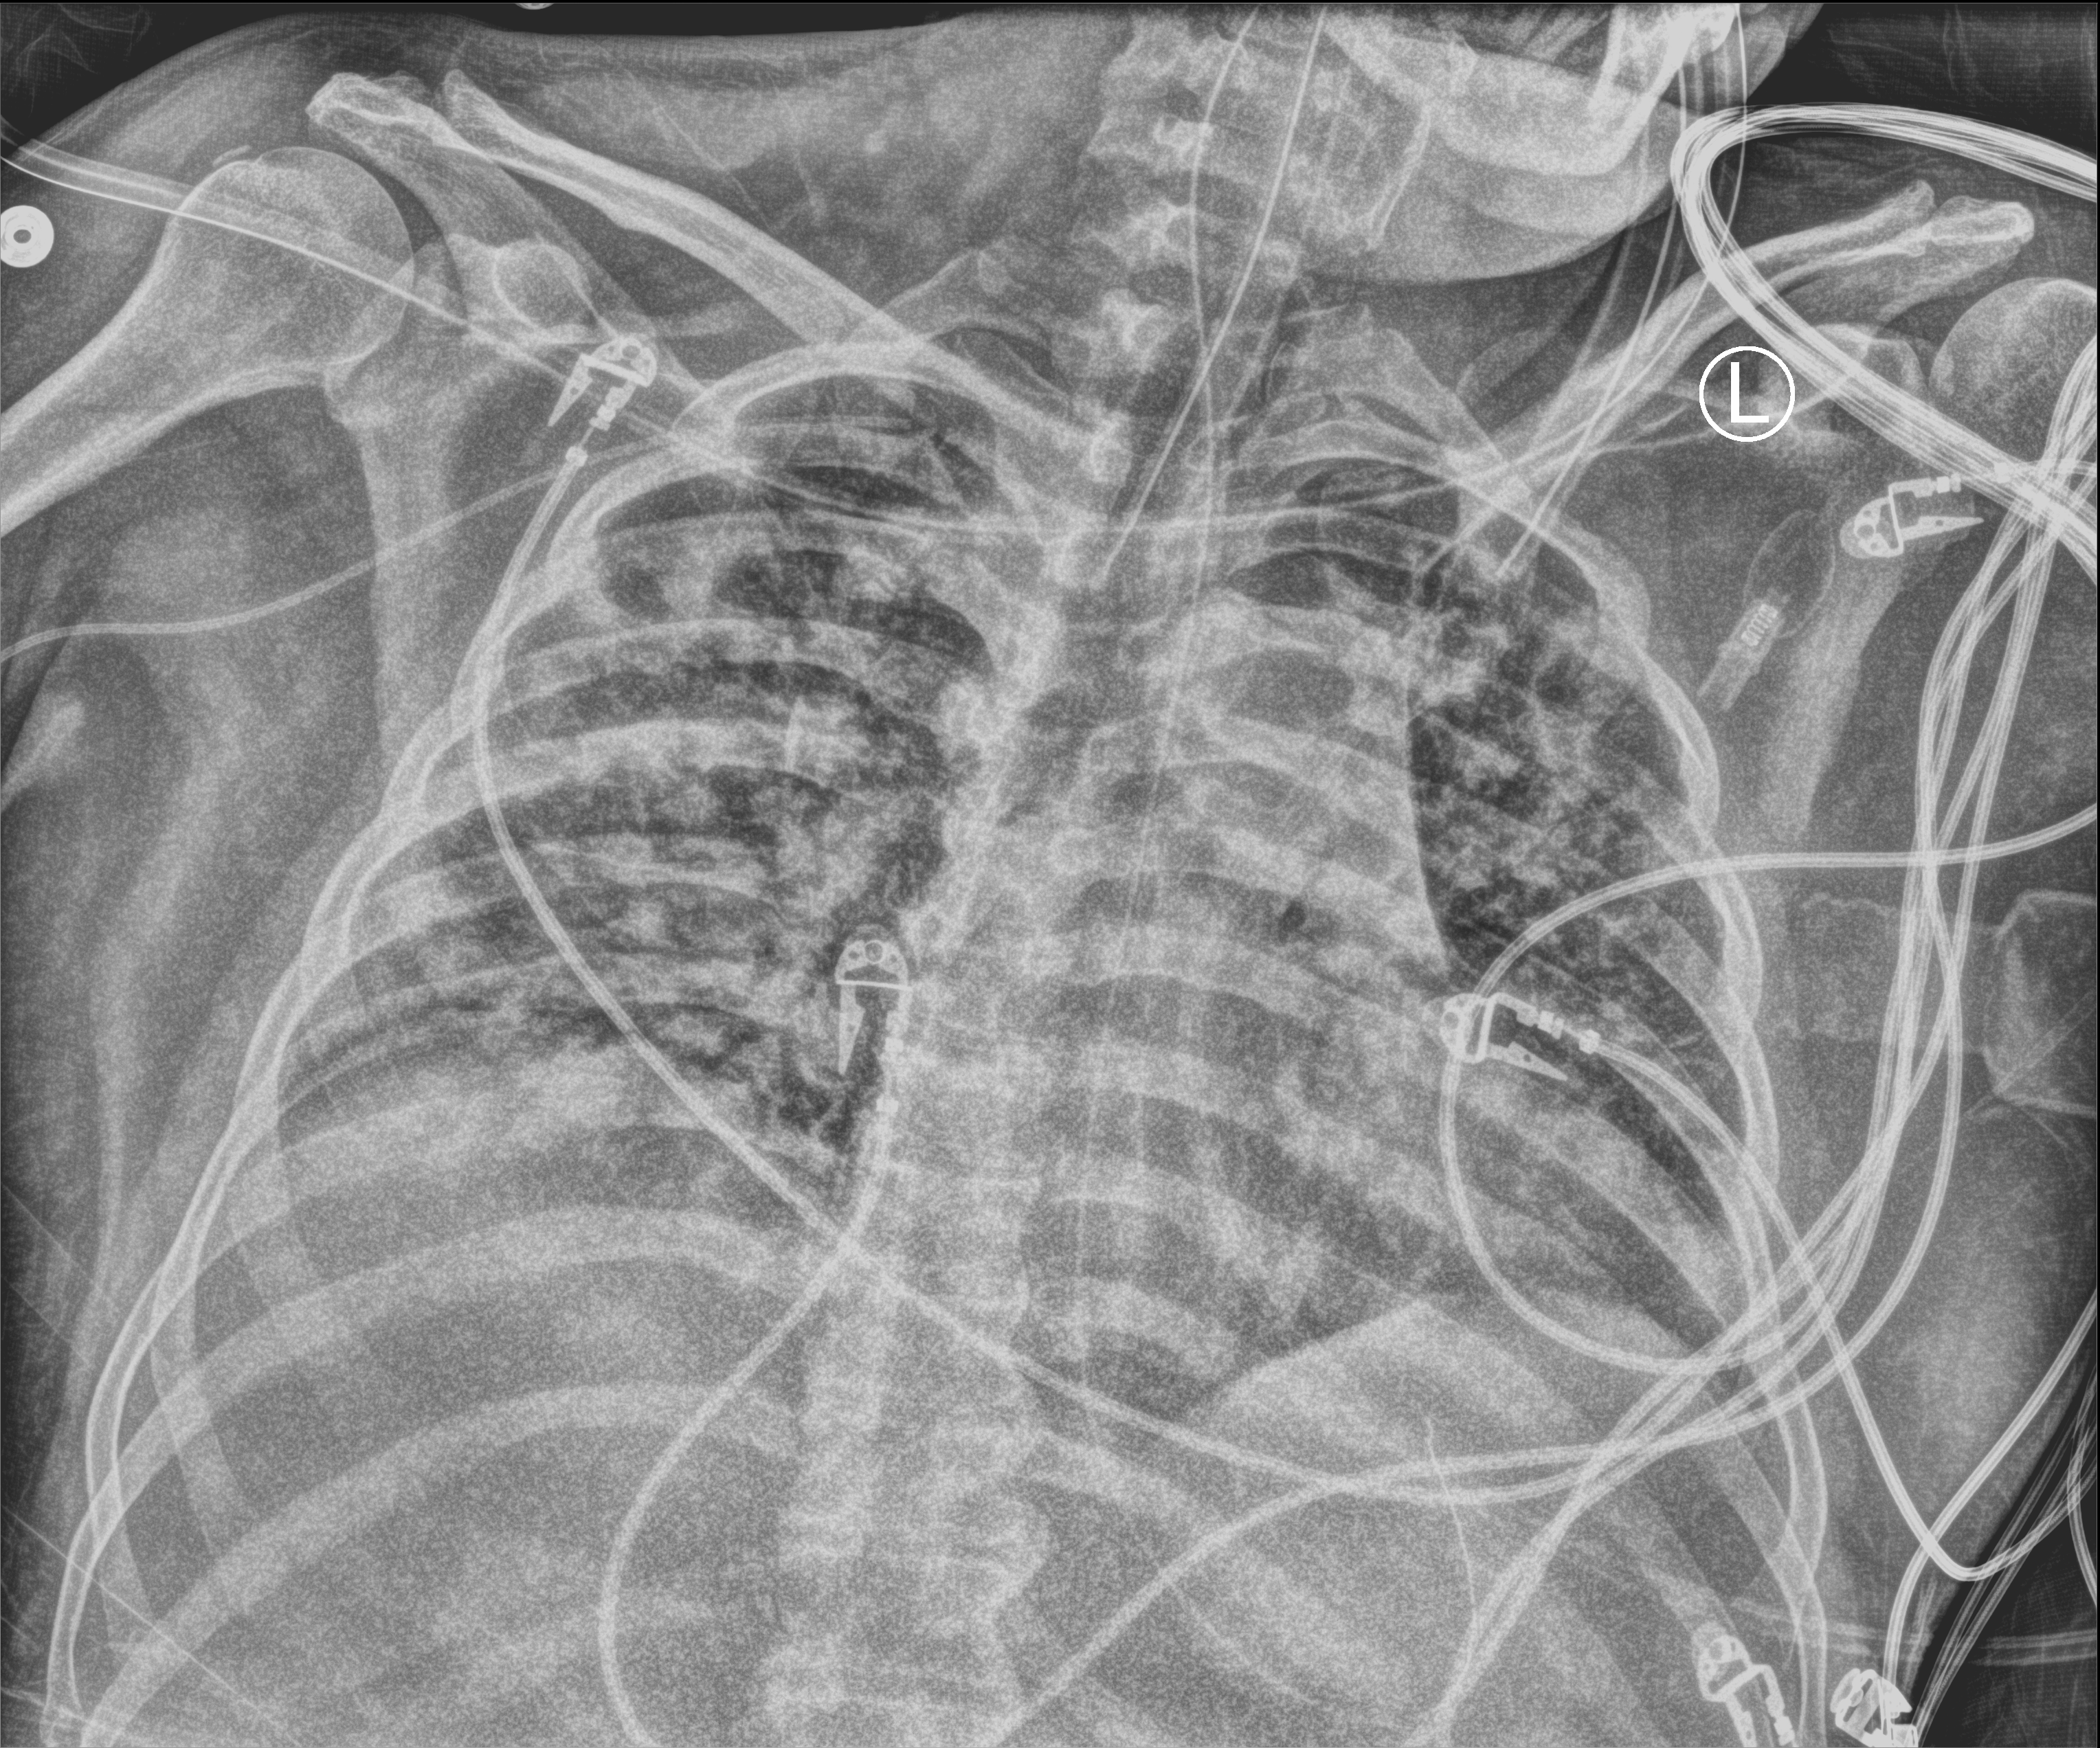
Portable chest radiograph. Patient hospitalised with COVID-19; male, aged 18–59 years.
Hospital-stay facts (about this admission, not read from this image; timing relative to this image not recorded):
- admitted to intensive care during this hospital stay: yes